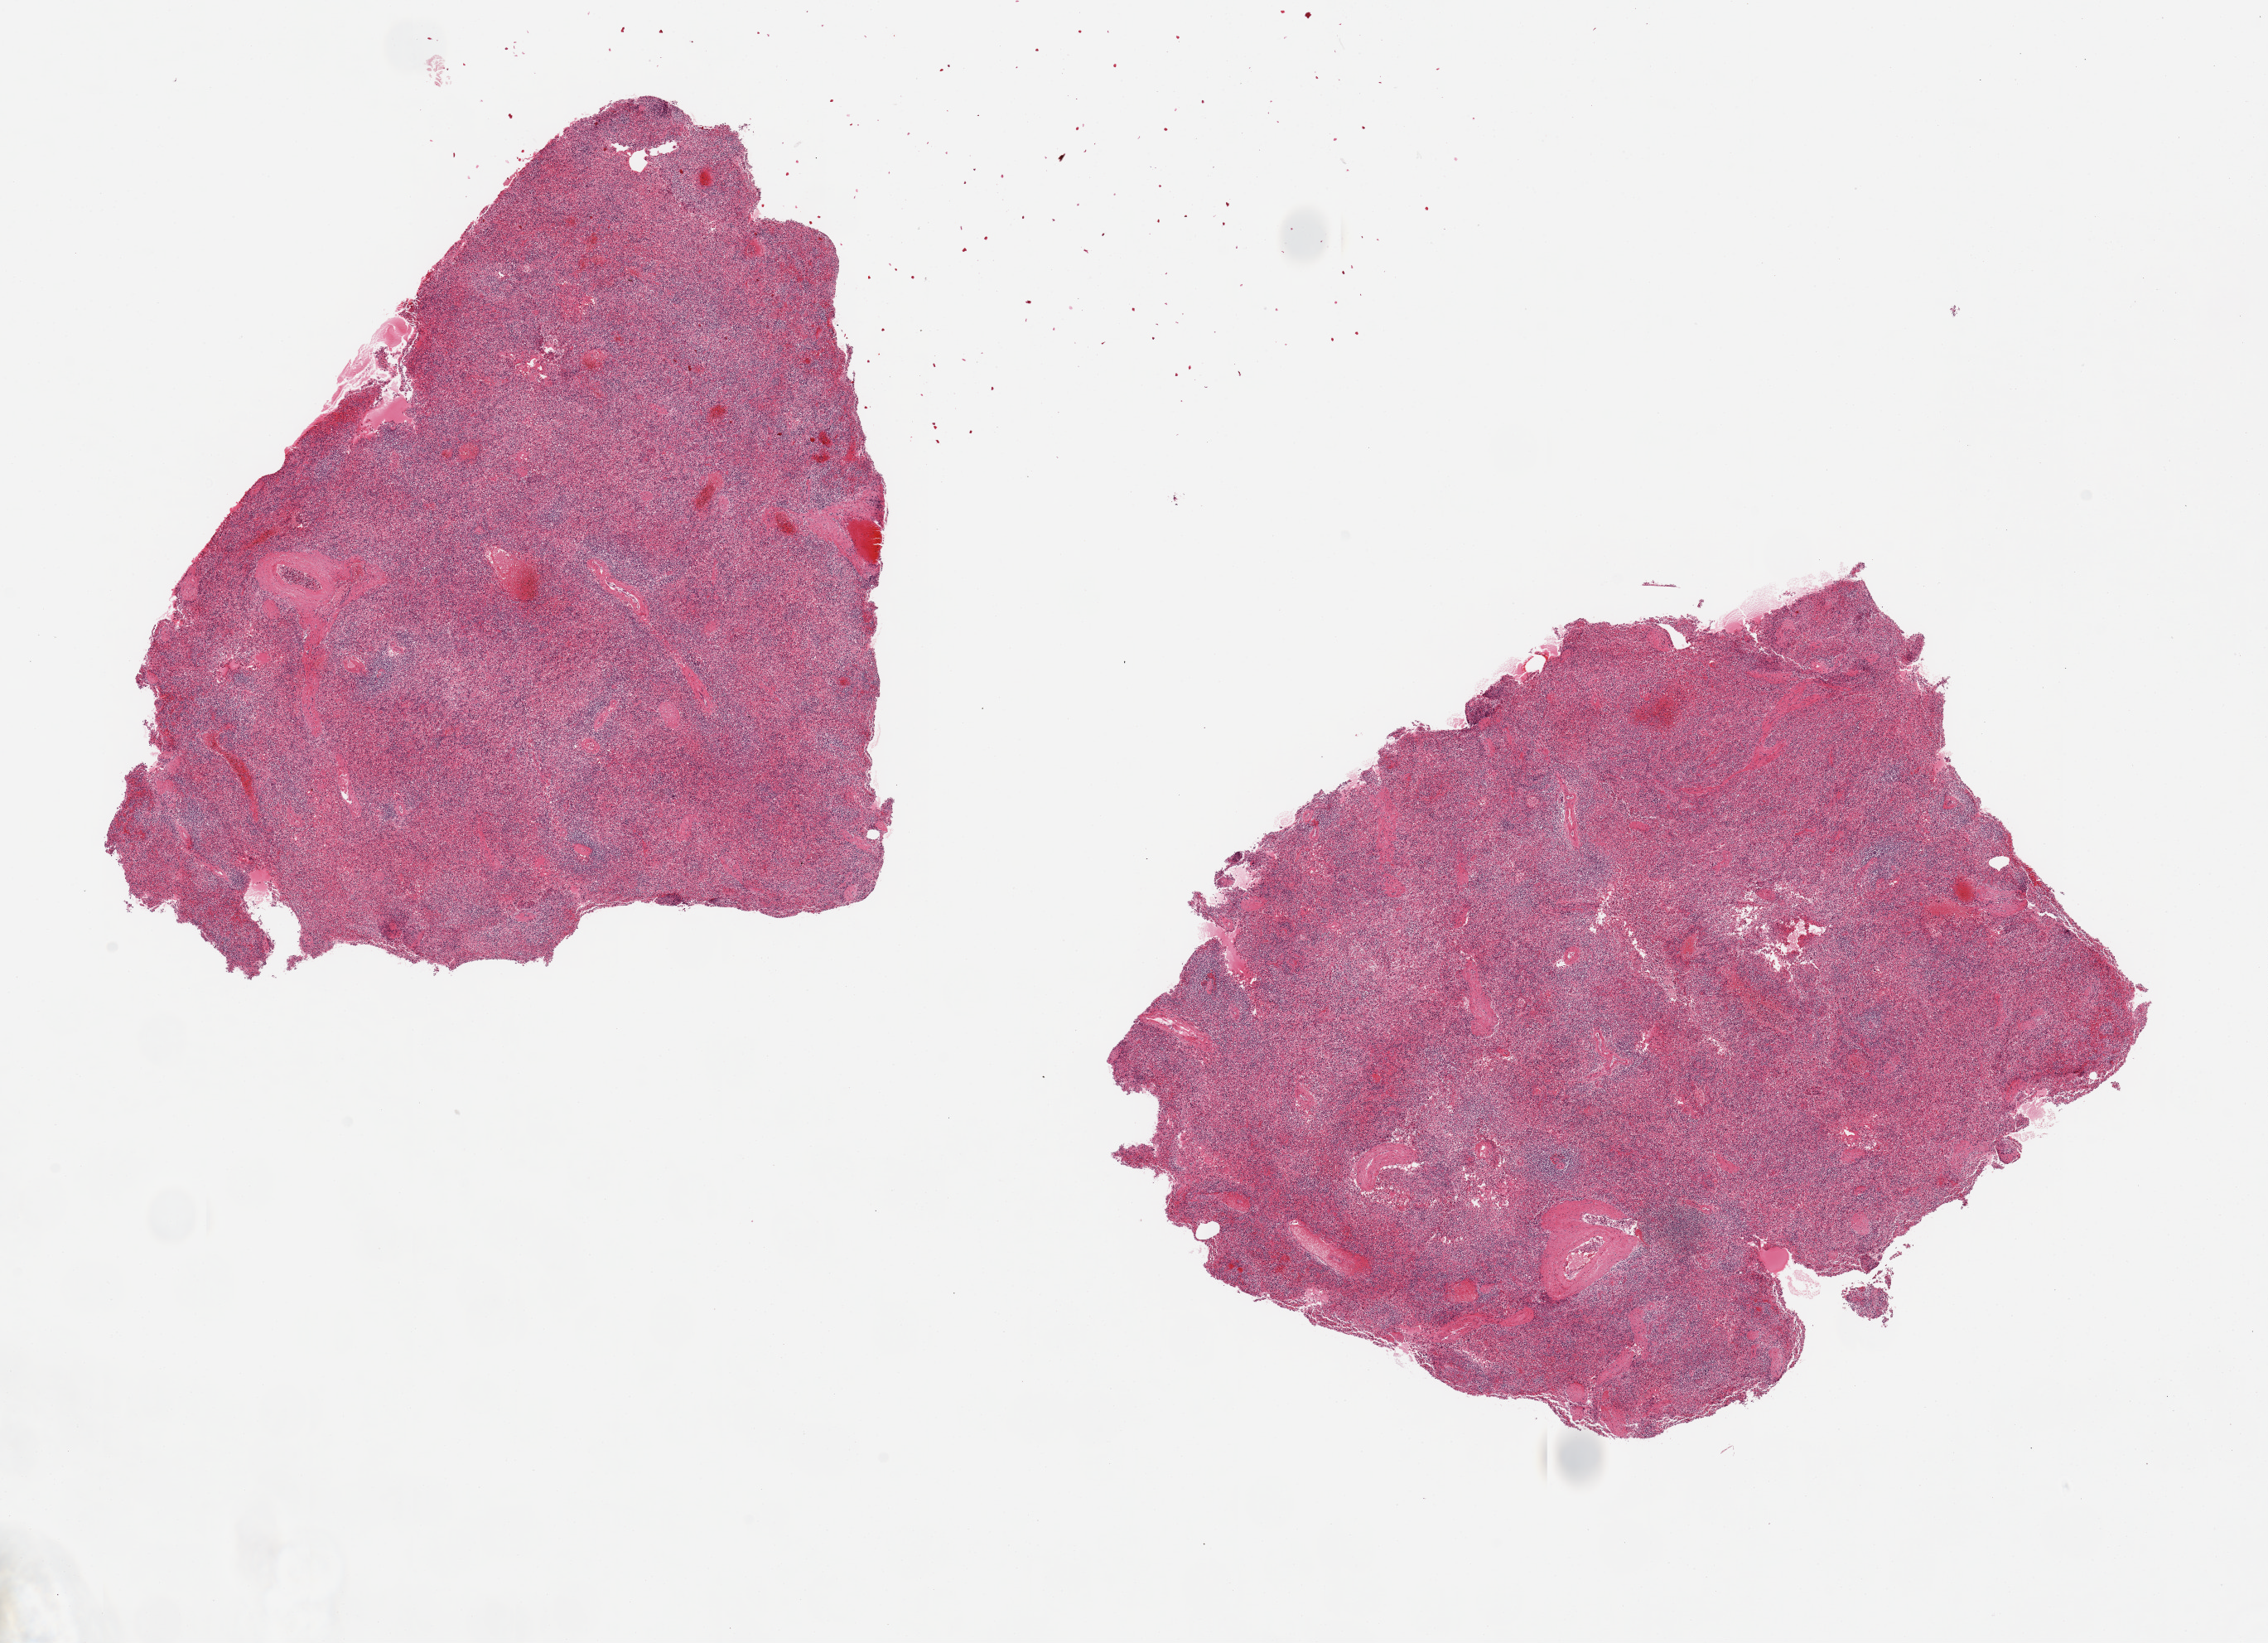
Whole-slide image, hematoxylin and eosin (H&E) stain — shown as a low-resolution overview of the whole scanned area (about 21.7 x 15.7 mm, from a 20x scan), PAXgene-fixed paraffin-embedded (PFPE) section, sampled site (target tissue): spleen, tissue donor sample.
* review note (as recorded): 2 pieces